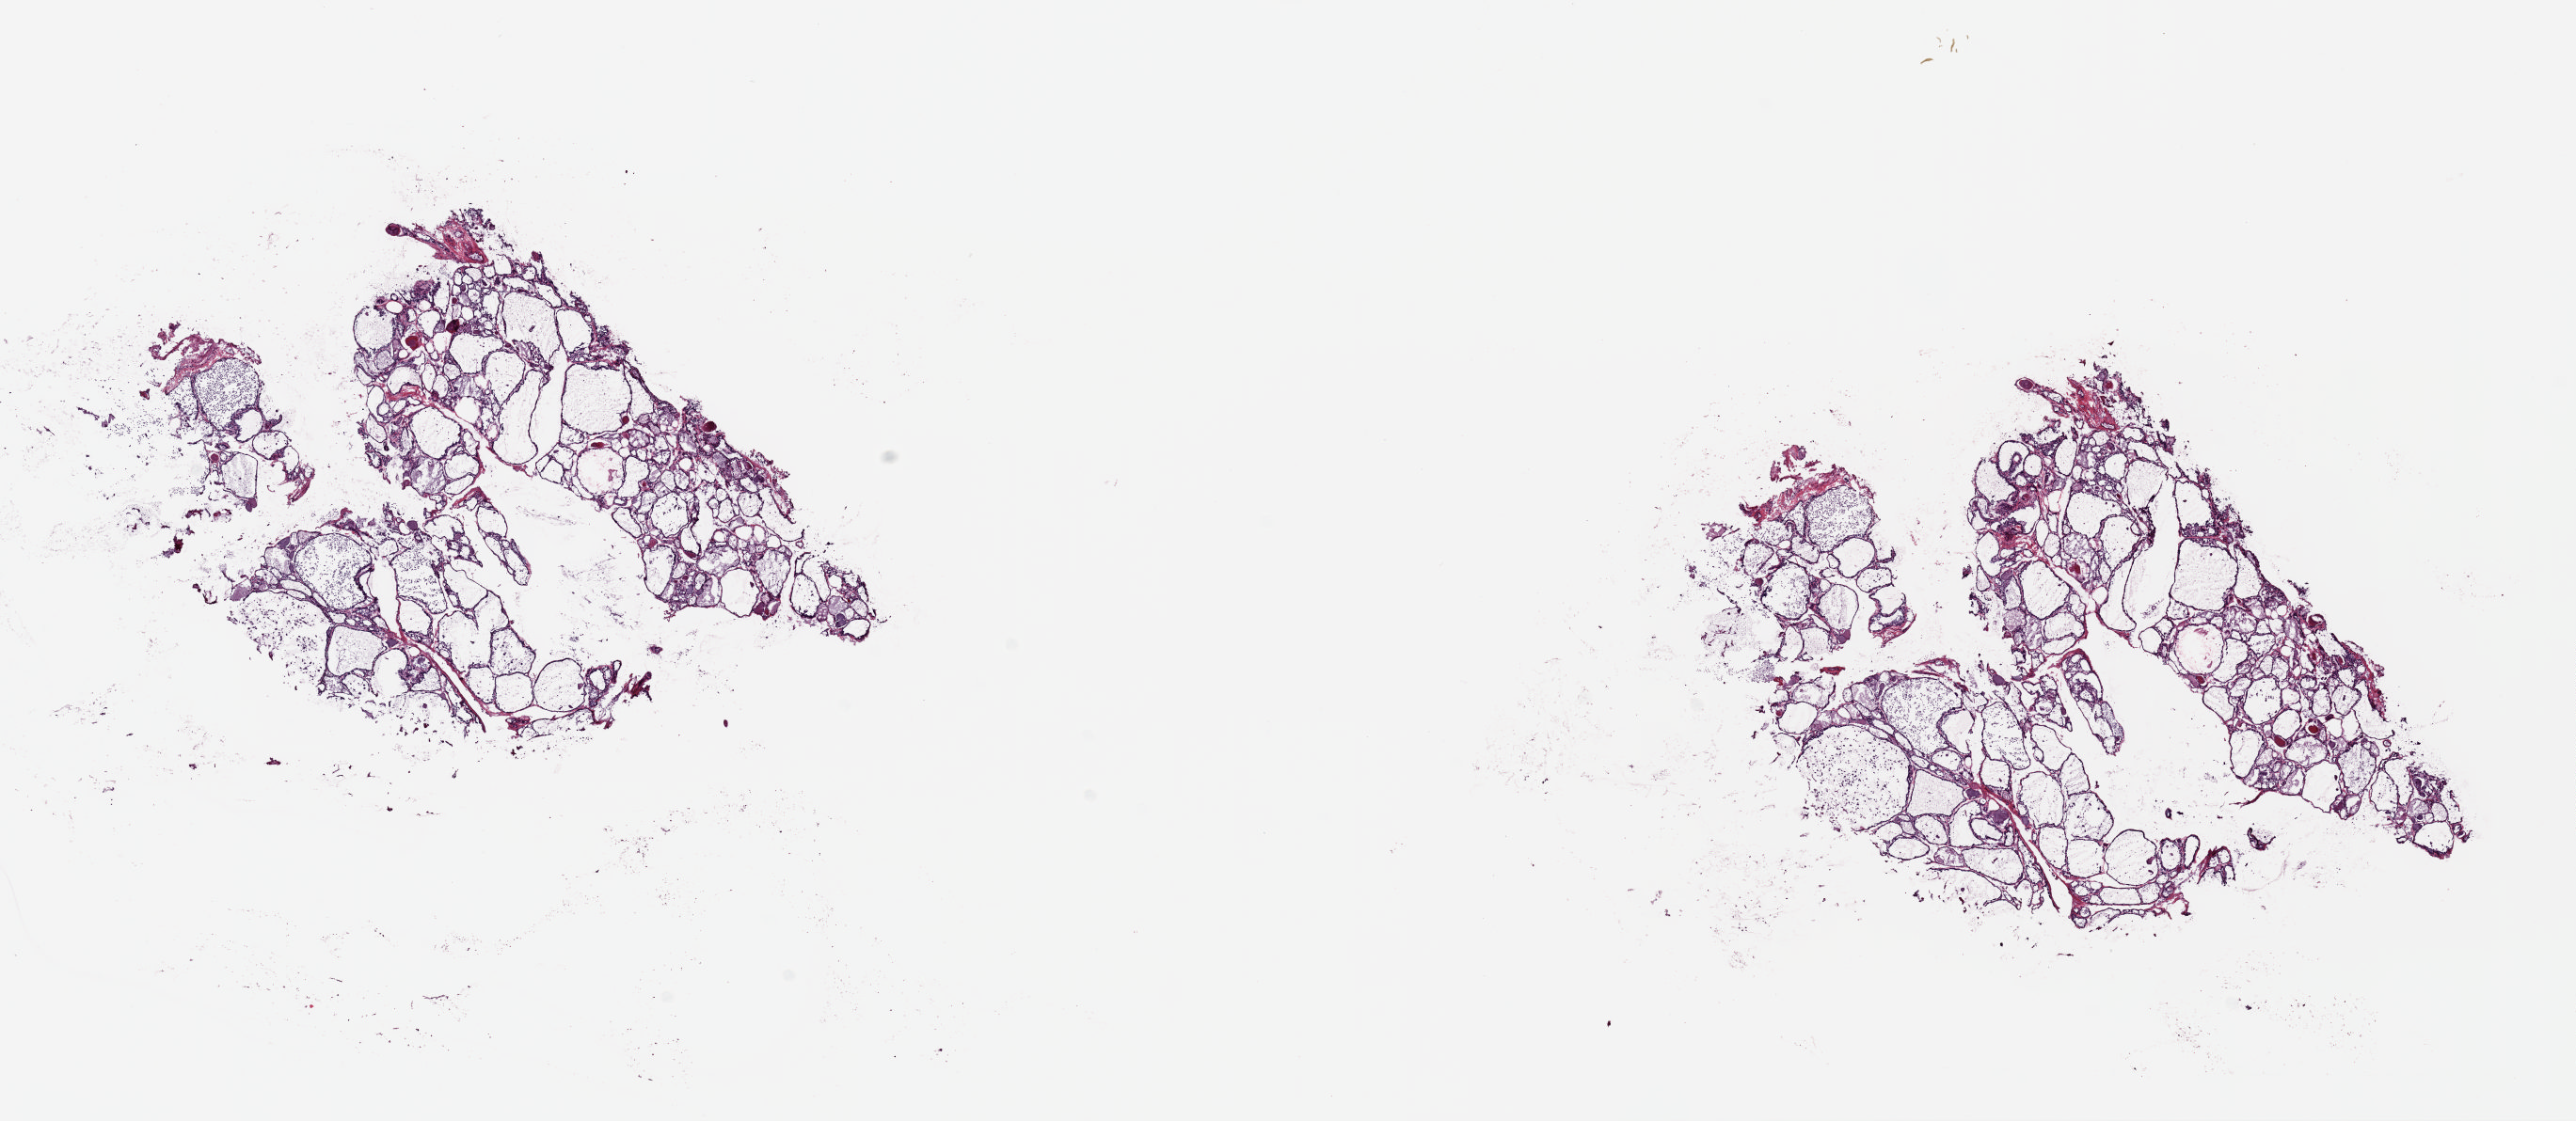
Whole-slide histology image, H&E-stained — low-resolution overview of the scanned area, about 21.6 x 9.4 mm. Frozen section. Sample: solid tissue normal (non-tumour tissue), thyroid. Male, age 60 years at initial diagnosis. Composition of this section per pathologist review: tumour cells 0%, tumour nuclei 0%, normal cells 100%, stromal cells 0%, necrosis 0%. Infiltration values recorded for this section: lymphocyte infiltration 1%, monocyte infiltration 5%, neutrophil infiltration 0%.
* this section: solid tissue normal (non-tumour) sample from the same patient
* patient diagnosis: Papillary adenocarcinoma, NOS (thyroid gland)